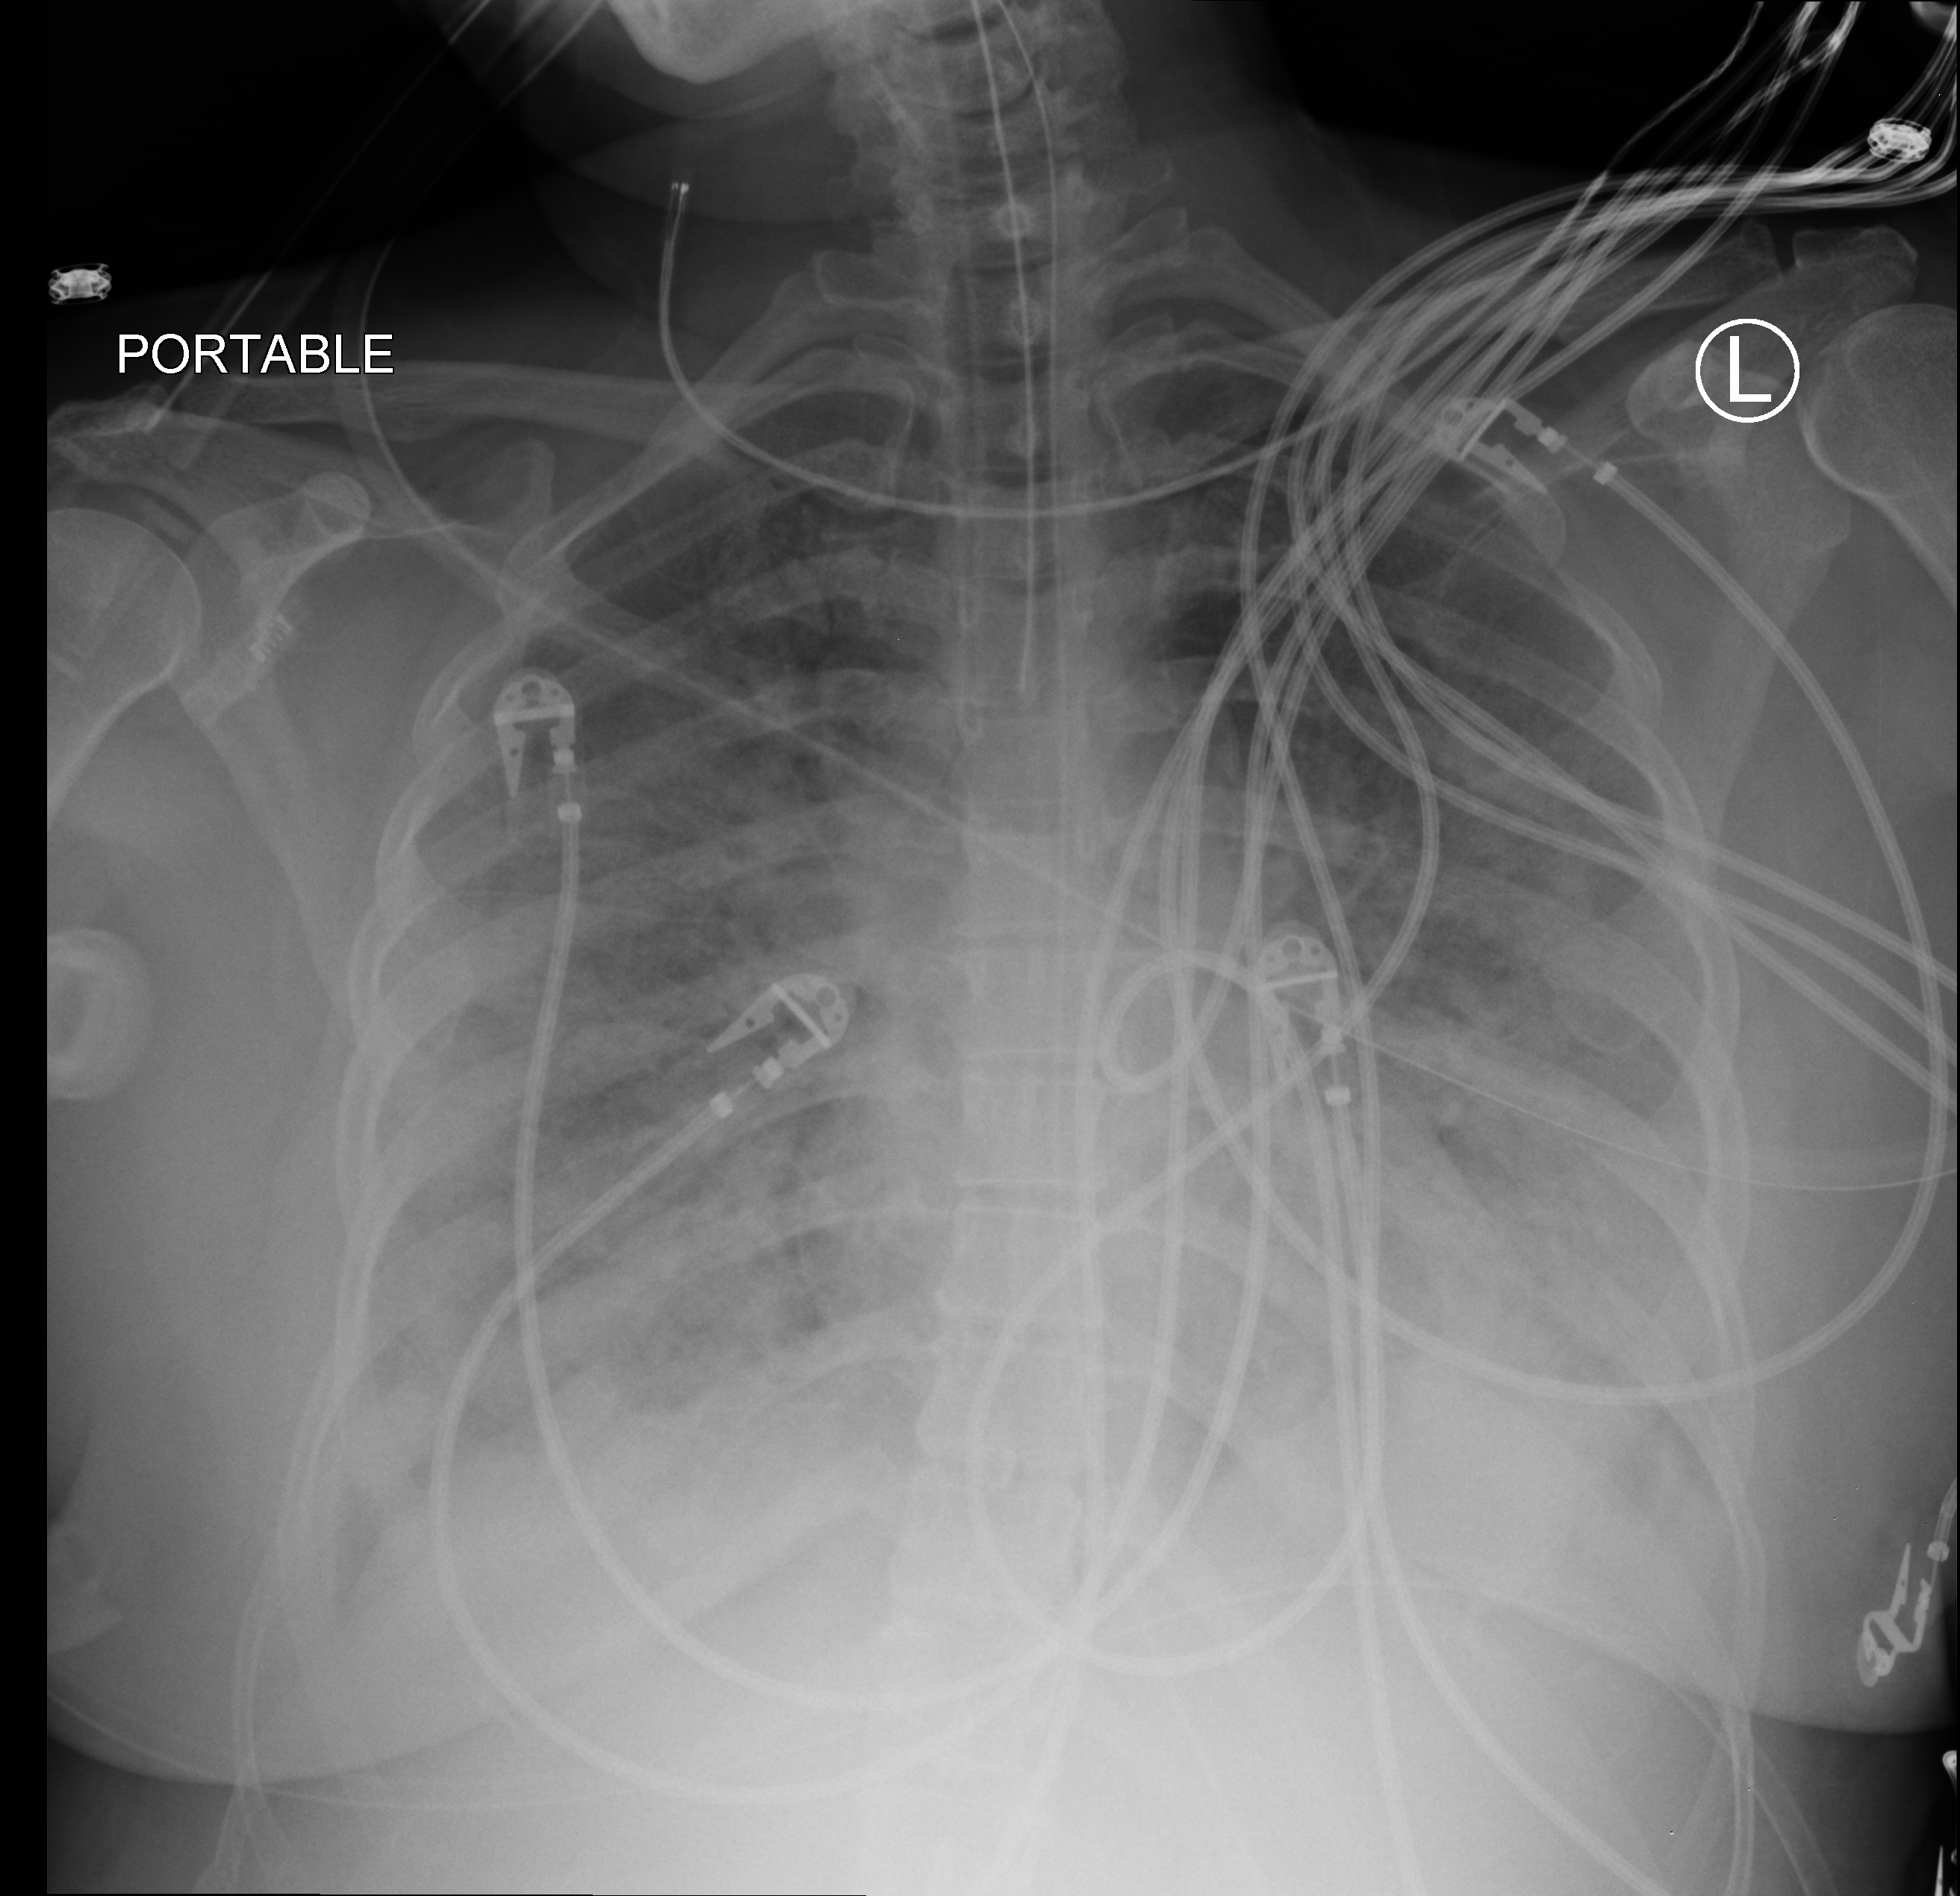
Bedside chest radiograph (computed radiography); anteroposterior (AP) projection. Patient hospitalised with COVID-19; male, aged 18–59 years.
From the hospital-stay record, not from the radiograph (when in the stay this image was taken is not recorded):
- admitted to intensive care during this hospital stay: yes